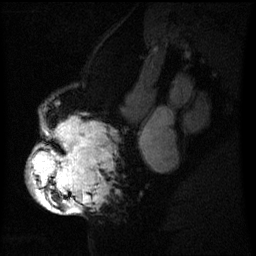
Breast MRI (dynamic contrast-enhanced), one sagittal slice; position 34 of 60 along the scan axis; dynamic contrast-enhanced series, image 2 of 3 at this slice position (ordered by acquisition); 1.5 T; TE 4.2 ms, TR 8 ms; 256 × 256 image matrix. Female patient, age 50 years.
Outlined on this slice (semi-automatically segmented with operator editing):
- analysis volume of interest (the breast-tissue region the enhancement analysis was run in; not a lesion): bounding box (x1, y1, x2, y2) in pixels: (29, 116, 109, 211)
- tumour enhancement mask (voxels above the 70 % enhancement threshold inside the analysis volume of interest): (30, 120, 102, 211)